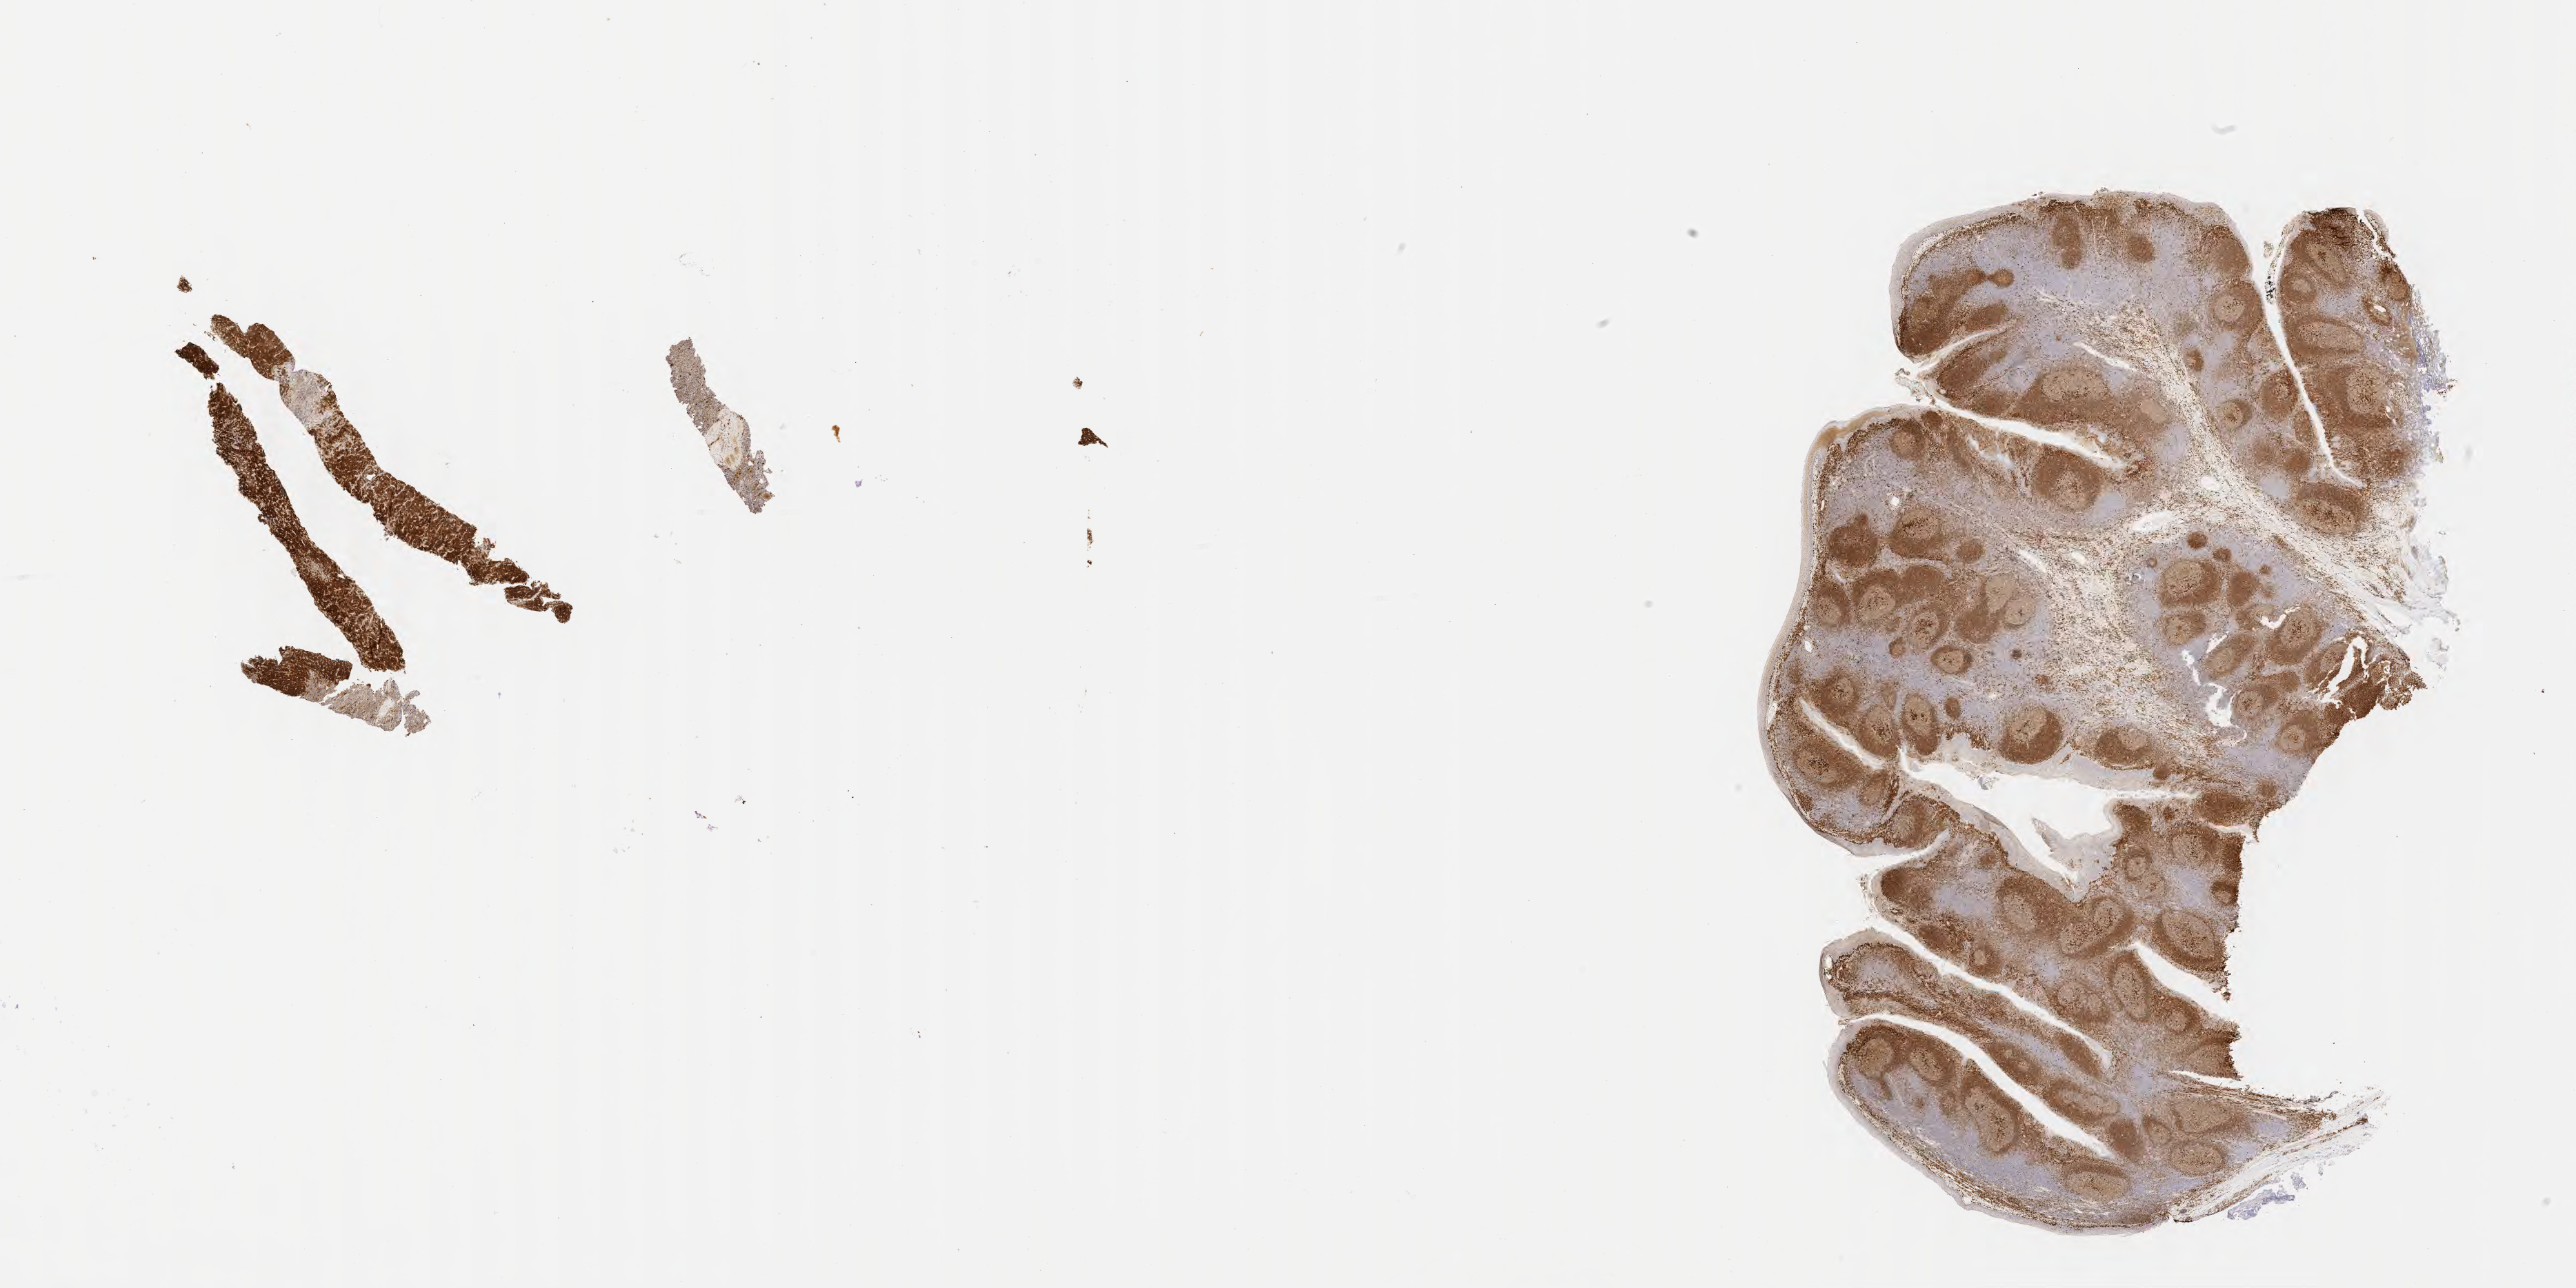
IHC for CD79a, whole-slide image, a low-resolution overview of the entire scanned area, about 30.2 x 15.1 mm; specimen: tumor tissue. Patient: male, aged 13.
Histologic diagnosis: Diffuse large B-cell lymphoma, NOS.